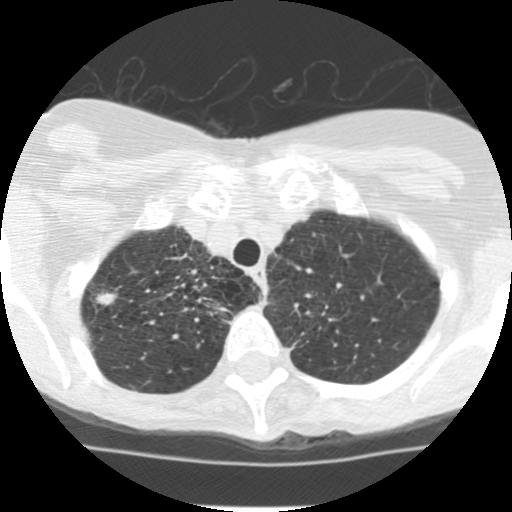
Low-dose screening chest CT, axial slice, baseline annual screen, lung window (W 1500 / L -600 HU), 2.5 mm slice thickness, standard (soft-tissue) reconstruction kernel (STANDARD), slice 25 of 135 in the series, 512 × 512 image matrix, field of view 280 × 280 mm. Female, age 68 years at enrolment. Current smoker at enrolment.
- Lesion marked by an expert reader, bounding box <69,278,128,328> (left, top, right, bottom; pixels).
- The screening reader recorded 2 non-calcified nodules or masses ≥4 mm on this exam (right upper lobe, right upper lobe); which of them this box marks is not recorded.
- Official screen result: positive, change unspecified: nodule(s) >= 4 mm or enlarging nodule(s), mass(es), or other non-specific abnormalities suspicious for lung cancer.